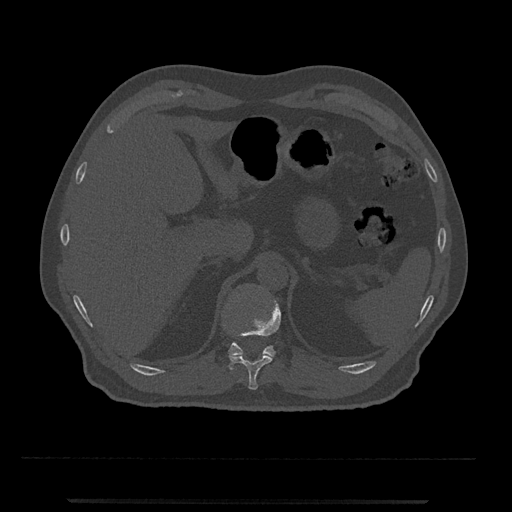
CT including the spine, one axial slice; slice 439 of 797 in the series (ordered by position); reconstruction kernel Br40s/3; bone window (W 1800 / L 400 HU); 0.5 mm slice thickness; 512 × 512 image matrix. Male patient, age 63 years. Case-level facts recorded for this patient, not image findings: primary cancer: prostate.
Outlined on this slice (semi-automatically segmented with operator editing):
- T11 vertebra: bounding box <229,300,281,390> (left, top, right, bottom; pixels)
- T12 vertebra: <228,342,276,370>